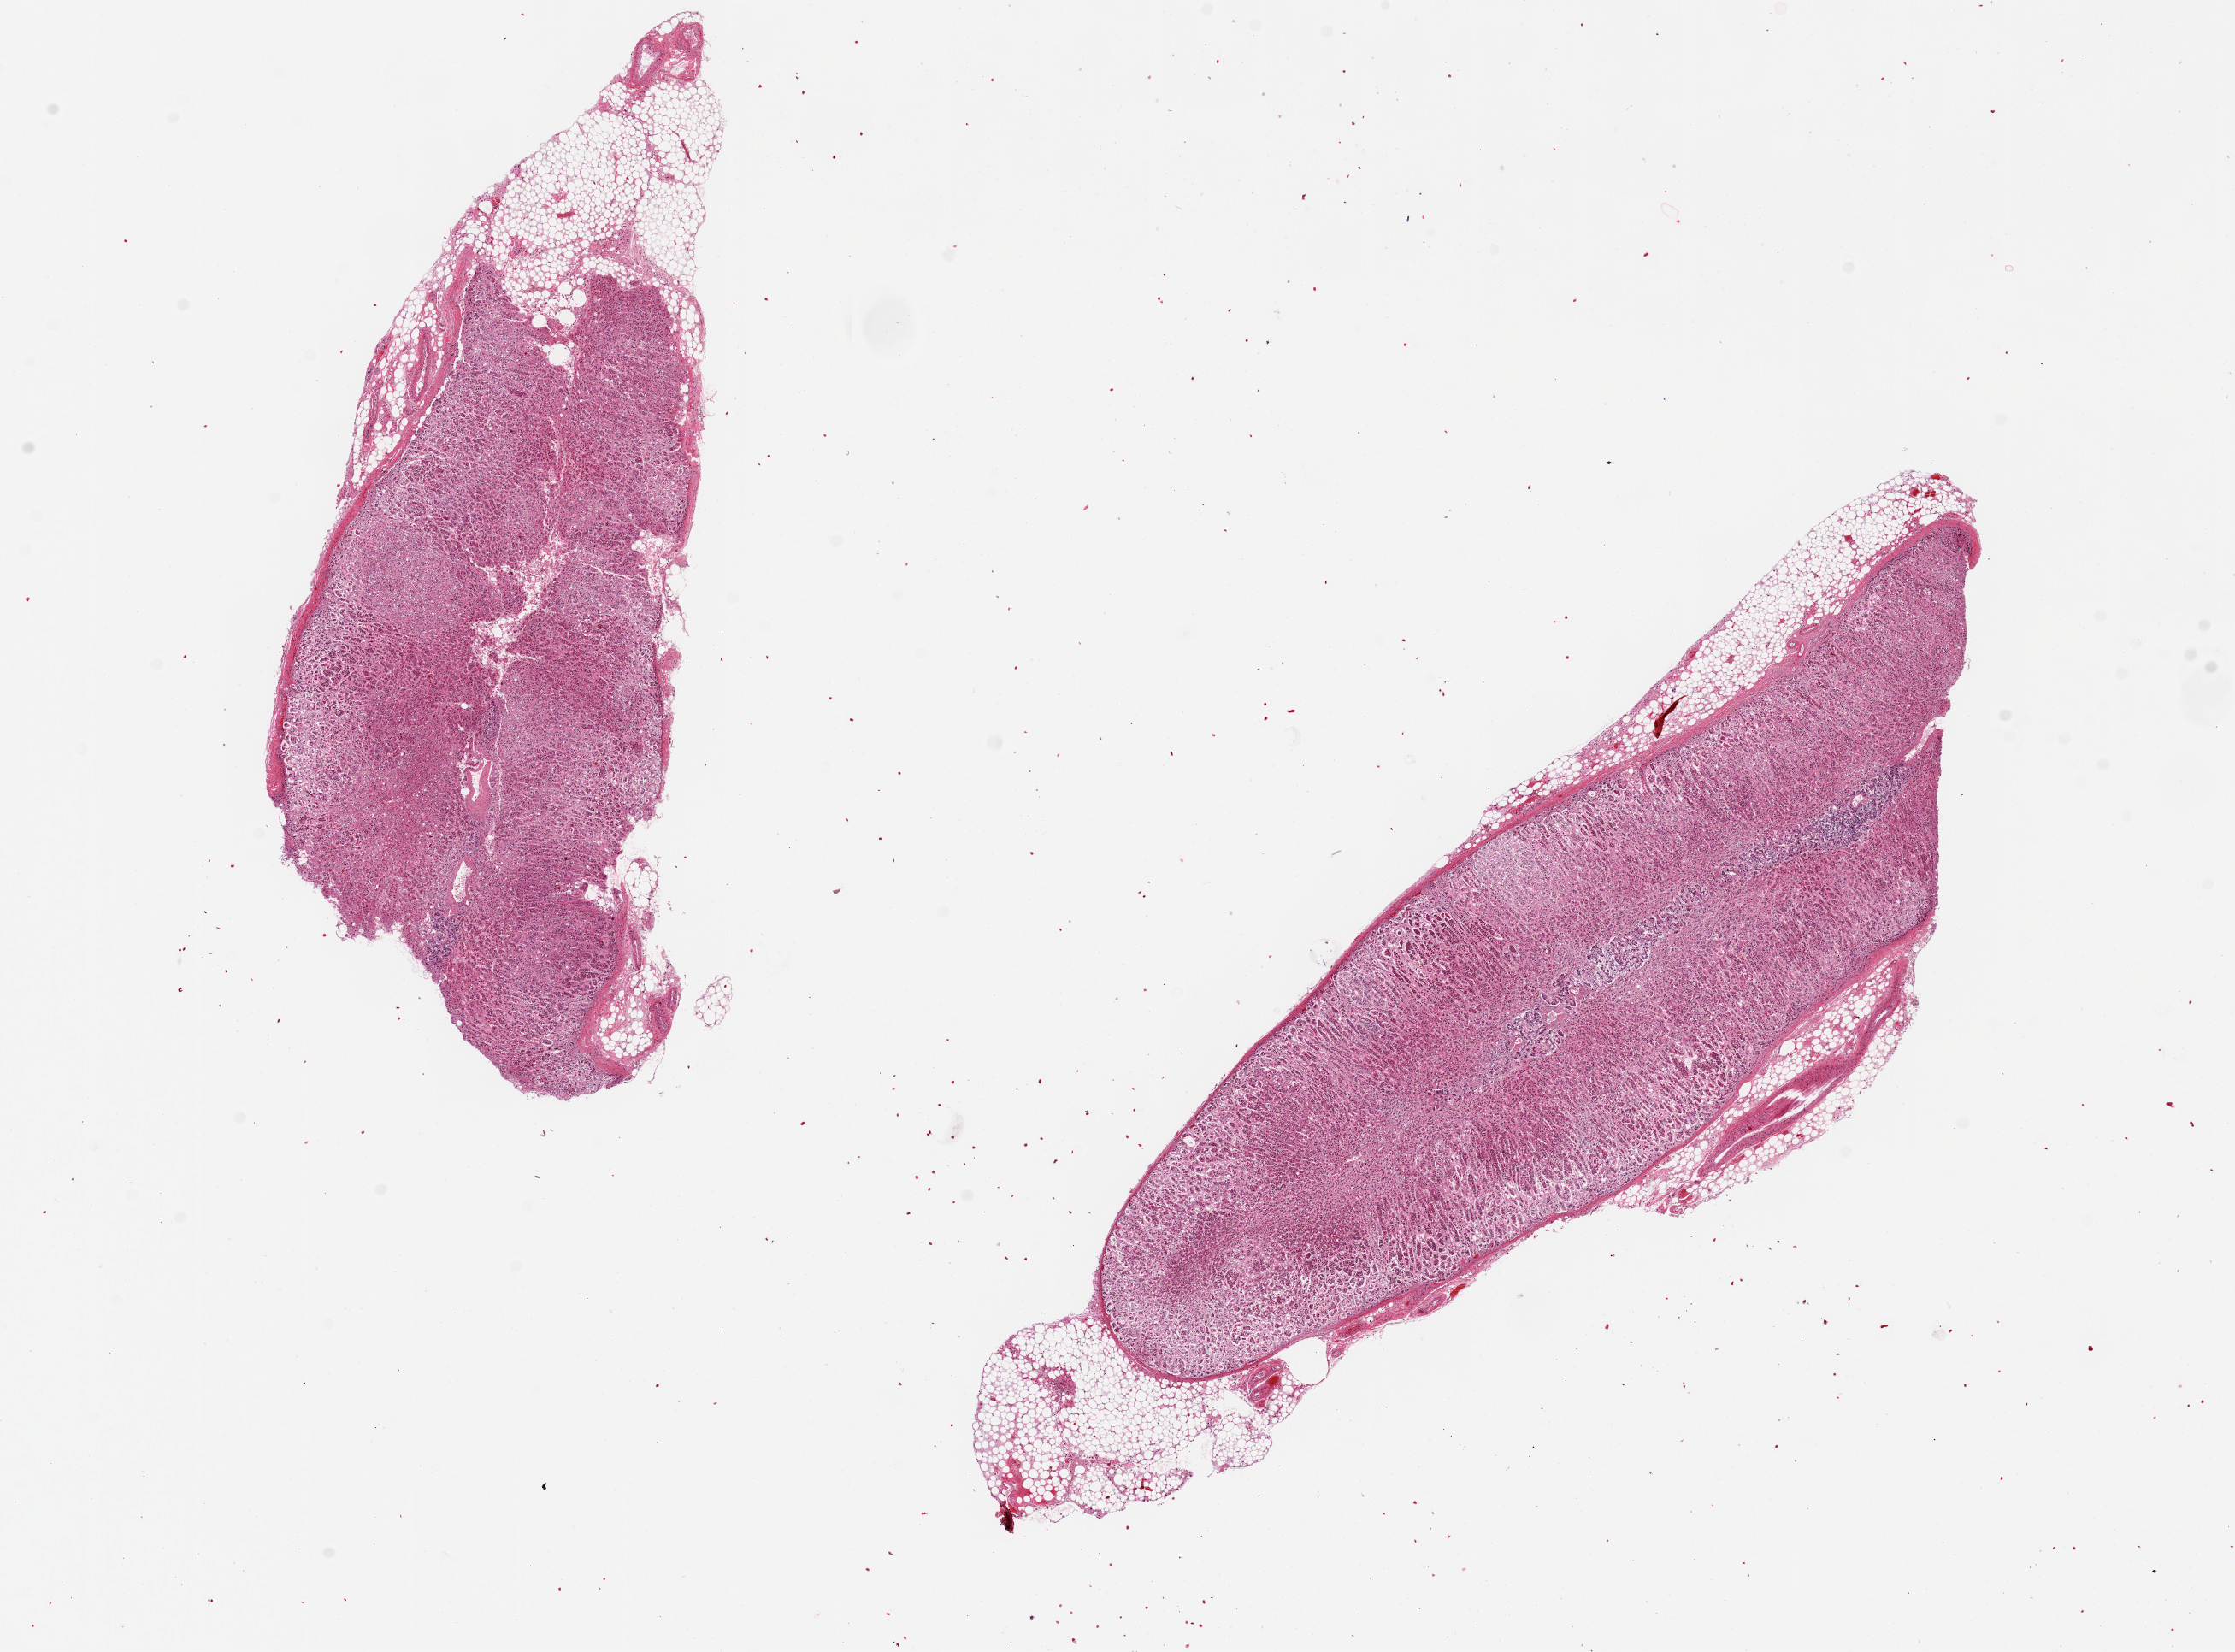
Digitized haematoxylin and eosin-stained section — low-resolution overview of the scanned area, about 20.7 x 15.3 mm (slide scanned at 20x), PAXgene-fixed paraffin-embedded (PFPE) section, sampled site (target tissue): adrenal gland, tissue donor sample. Donor: female.
Pathologist's review note for this sample: 2 pieces. 10x4 & 13x4mm; autolysis varies from 2-3; 20% external adipose.